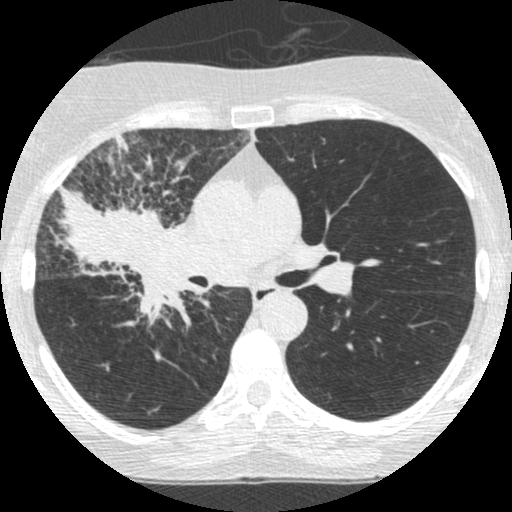
Low-dose screening chest CT, one axial slice; position 152 of 253 along the scan axis; reconstruction kernel STANDARD; lung window (W 1500 / L -600 HU); 1.25 mm slice thickness; 512 × 512 image matrix.
Annotated regions visible in this slice (expert manual segmentation):
- lesion 2 (tumor, hilum of right lung): bounding box <54,185,186,335> (left, top, right, bottom; pixels)